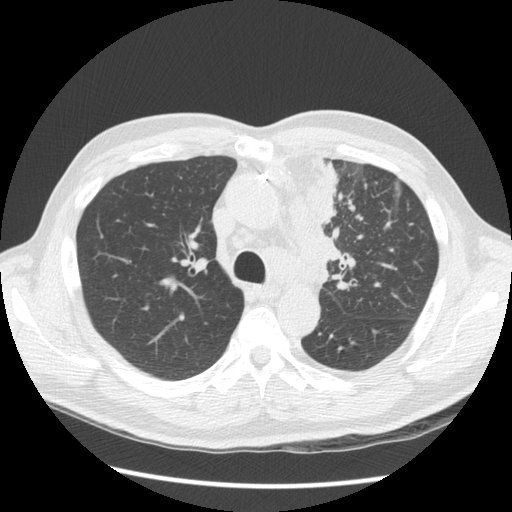
Low-dose screening chest CT, one axial slice; slice 96 of 136 in the series (ordered by position); 120 kVp; lung window (W 1500 / L -600 HU); 512 × 512 image matrix, field of view 360 × 360 mm.
Structures marked on this image (expert manual segmentation):
- lesion 1 (tumor, upper lobe of left lung): box from (x=291, y=154) to (x=335, y=289) px